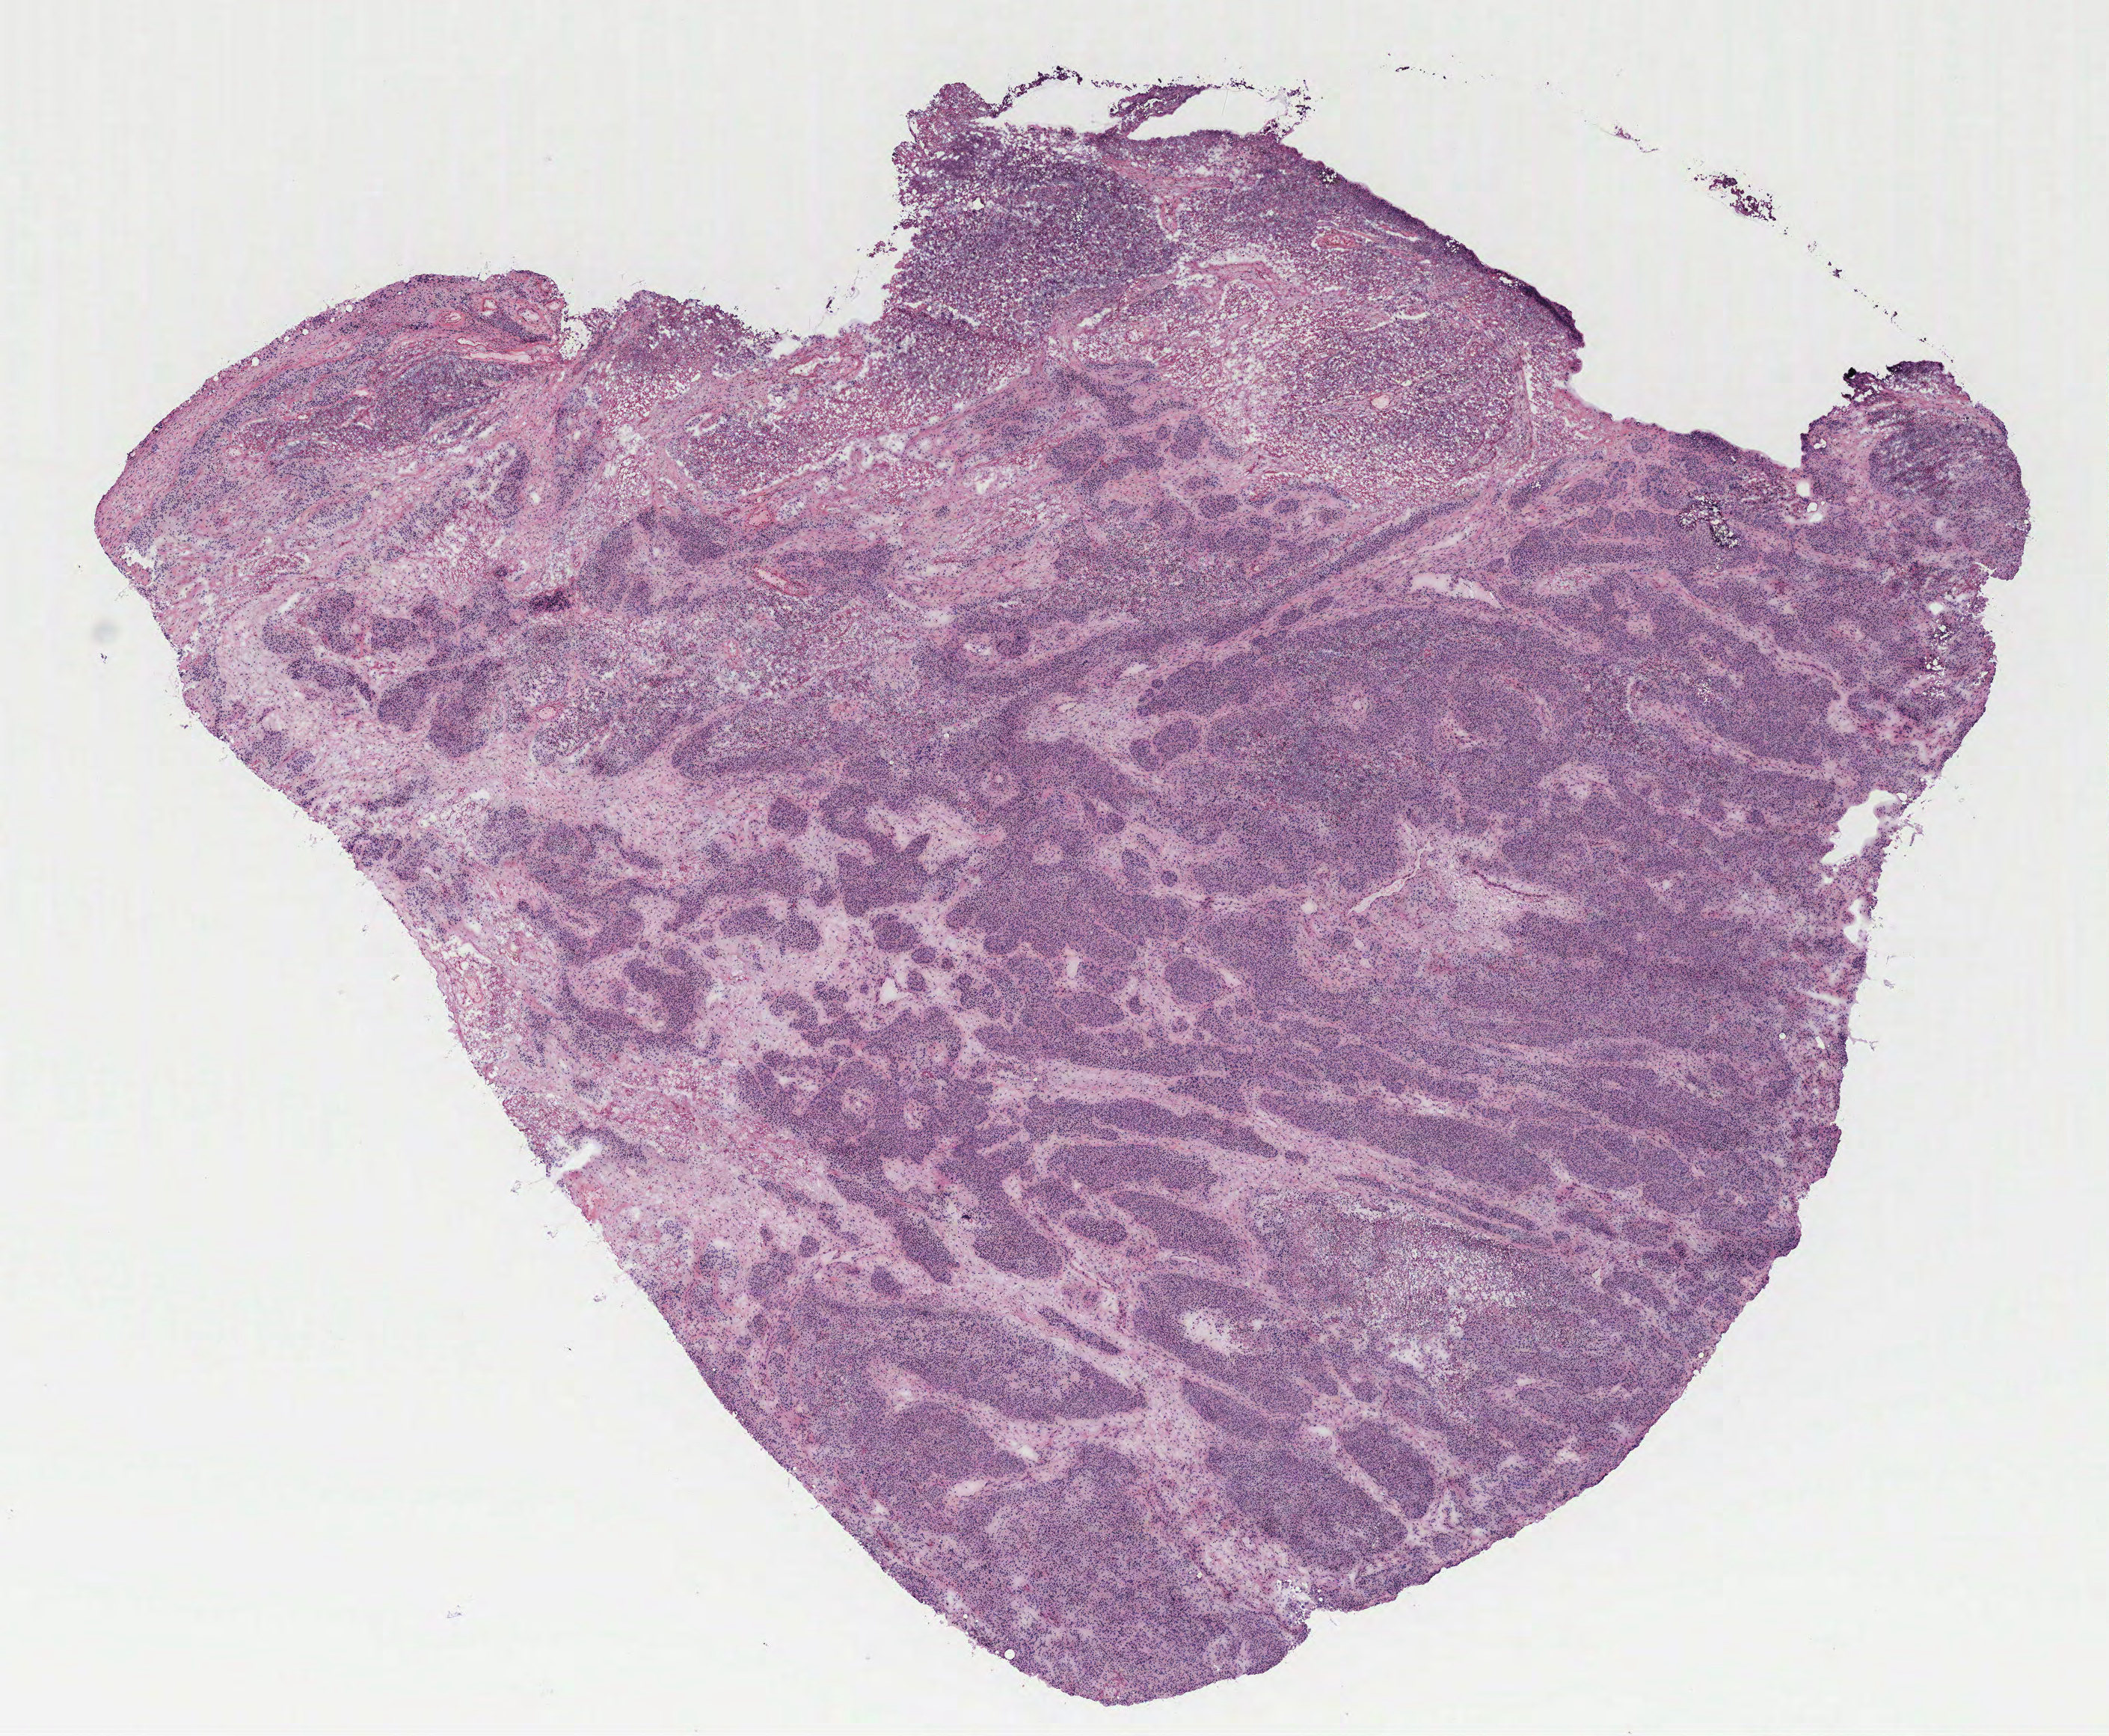
Whole-slide histology image, H&E-stained — whole scanned area (about 11.3 x 9.3 mm, from a 40x scan) shown as a low-resolution overview; ovary, tissue type not recorded. Female patient.
• patient diagnosis: Serous adenocarcinoma, NOS